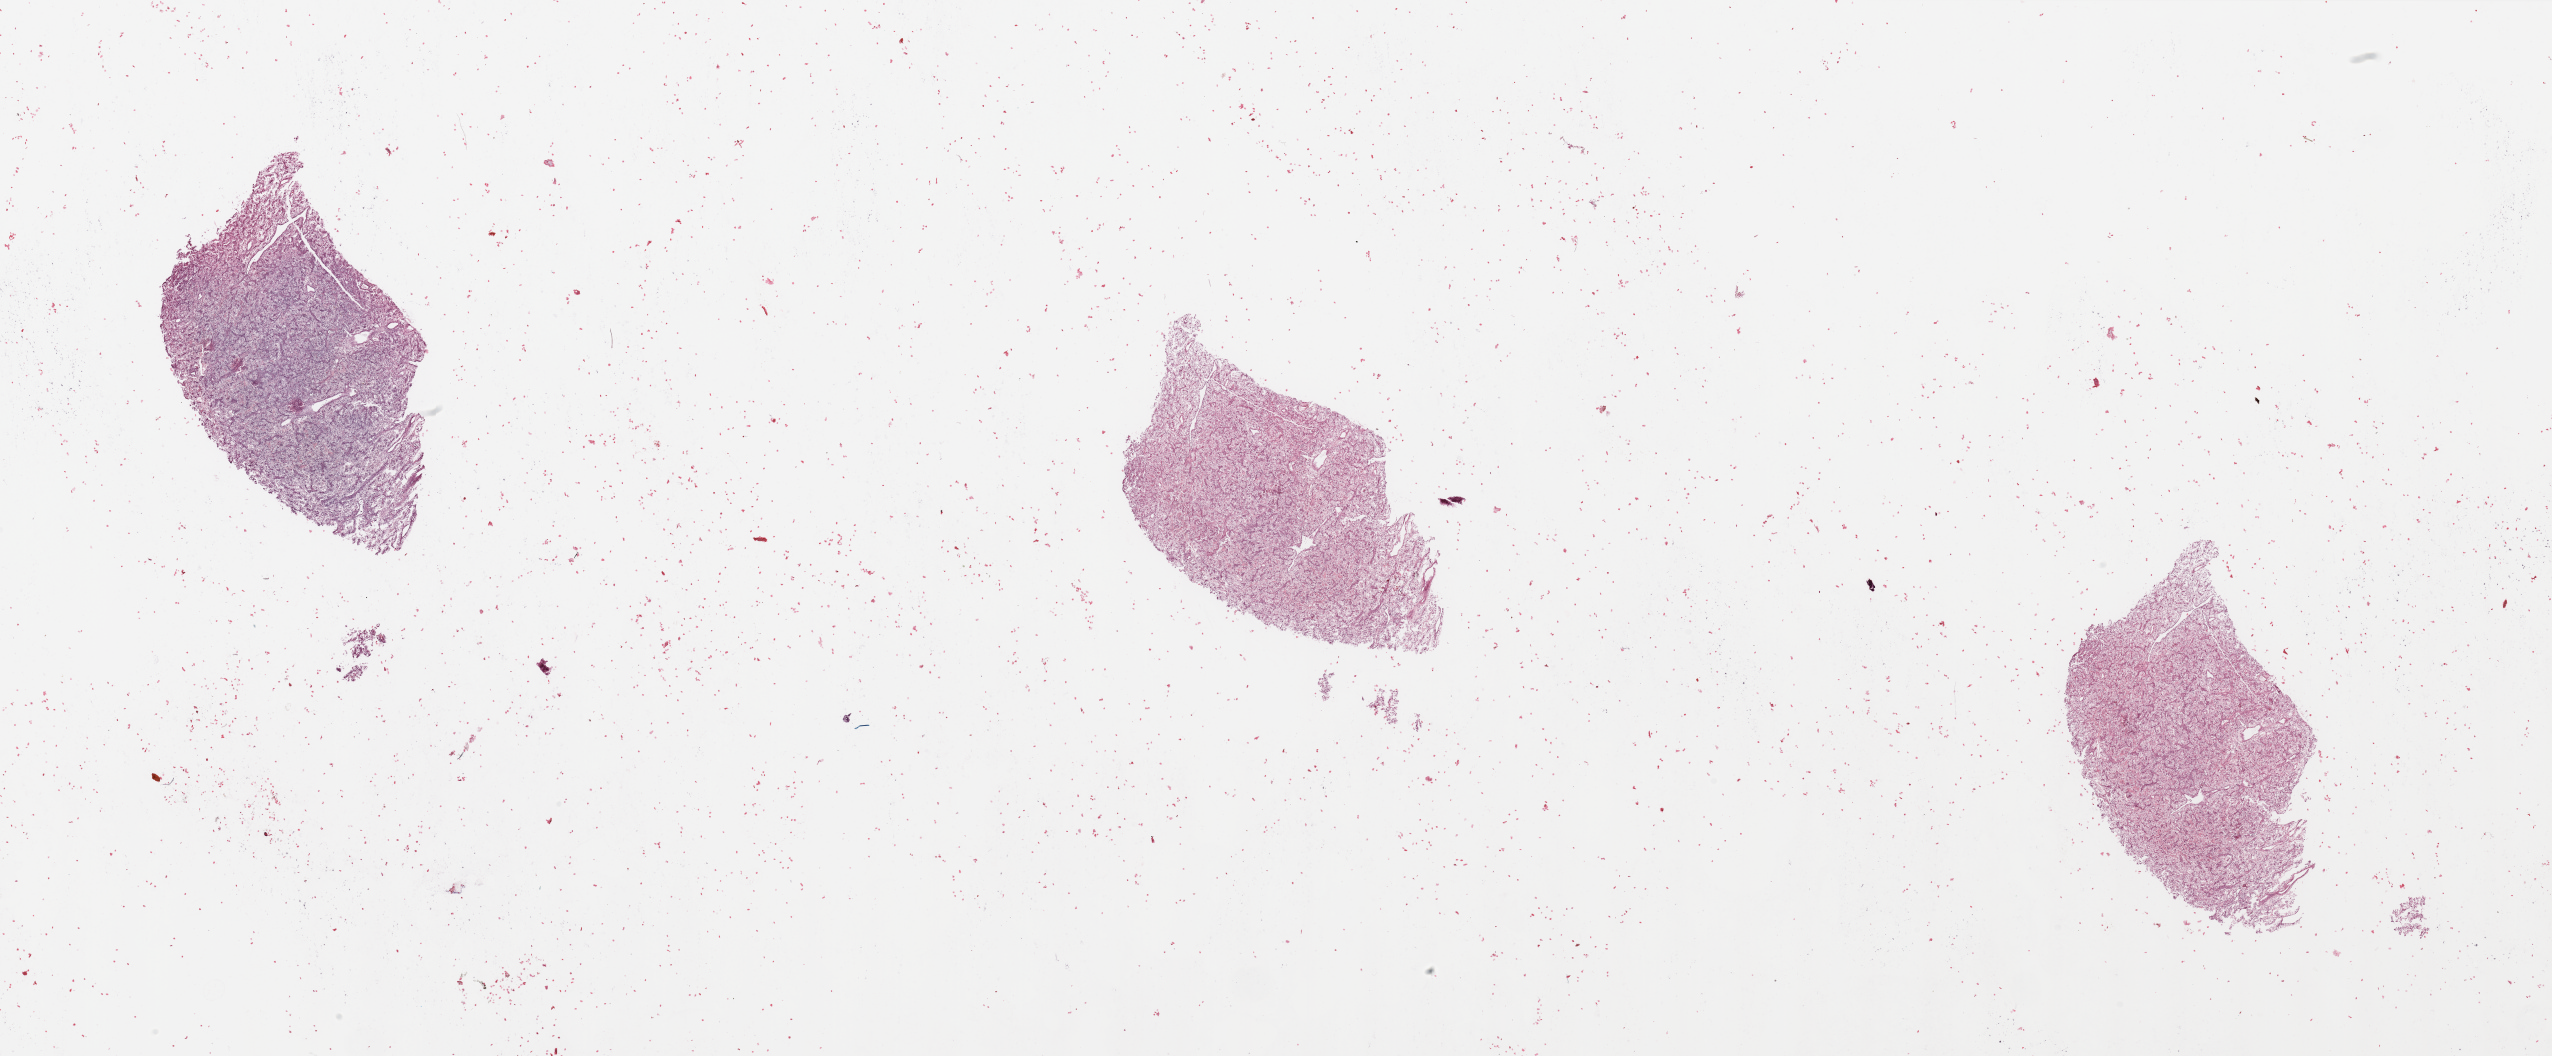
H&E whole-slide image — shown as a low-resolution overview of the whole scanned area (about 40.4 x 16.7 mm), kidney, tumour tissue. Patient: male, age 67 years. Histologic grade: G3 (poorly differentiated).
Primary tumour site (as recorded): middle. AJCC pathologic stage: I. Diagnosis: Renal cell carcinoma, NOS.